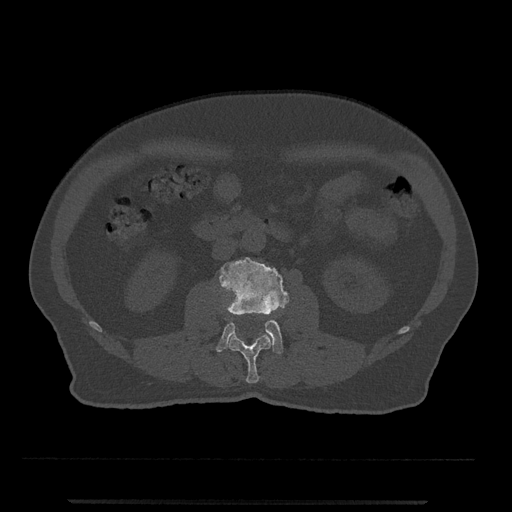
CT including the spine, one axial slice; position 233 of 797 along the scan axis; reconstruction kernel Br40s/3; 120 kVp; bone window (W 1800 / L 400 HU); 512 × 512 image matrix. Patient: male, 63 years. Case-level facts recorded for this patient, not image findings: primary cancer: prostate.
Structures marked on this image (semi-automatically segmented with operator editing):
- L2 vertebra: bounding box <228,333,272,383> (left, top, right, bottom; pixels)
- L3 vertebra: <216,257,289,354>